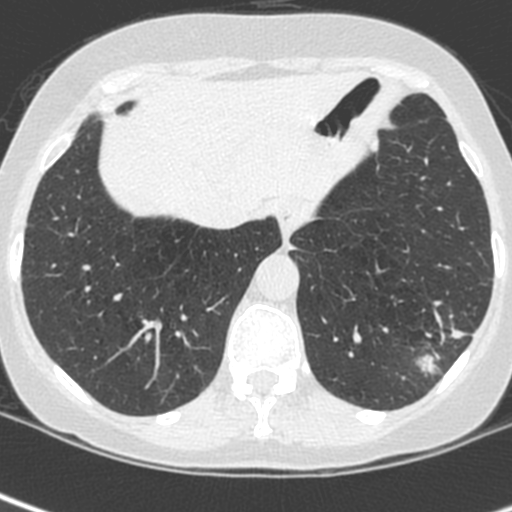
Chest CT (low-dose screening protocol), one axial image. Baseline screening round. Lung window (W 1500 / L -600 HU). 1.3 mm slice thickness. Standard (soft-tissue) reconstruction kernel (C). Slice 185 of 252 in the series. Female, age 56 years at enrolment.
• Expert-annotated lung lesion, bounding box [x1, y1, x2, y2] px = [398, 299, 482, 386].
• Reader record for this screening exam (exam-level; its link to the box is not recorded): non-calcified nodule or mass ≥4 mm, left lower lobe, 37 × 29 mm, spiculated (stellate) margins, ground glass attenuation.
• Official screen result: positive, change unspecified: nodule(s) >= 4 mm or enlarging nodule(s), mass(es), or other non-specific abnormalities suspicious for lung cancer.
• Participant outcome: lung cancer diagnosed 91 days after this screen — squamous cell carcinoma, NOS, left lower lobe, poorly differentiated (G3), stage IIIA (AJCC 6th edition), 35 mm at pathology.